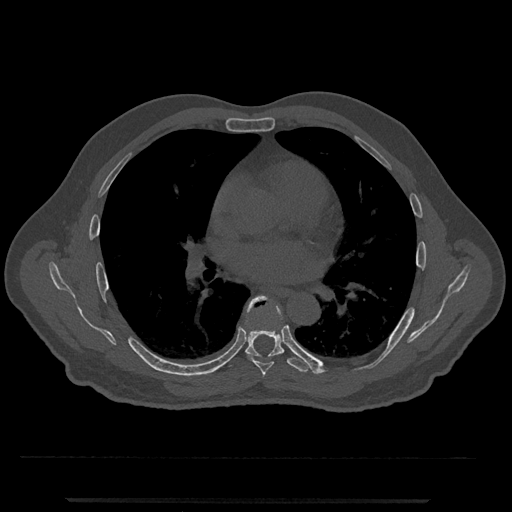
CT including the spine, one axial slice; position 711 of 797 along the scan axis; reconstruction kernel Br40s/3; 120 kVp; bone window (W 1800 / L 400 HU); 512 × 512 image matrix, field of view 419 × 419 mm. Male patient, age 63 years. From the clinical record (not read from this slice): primary cancer: prostate.
Annotated regions visible in this slice (semi-automatic segmentation, software-assisted and operator-edited):
- T6 vertebra: box from (x=245, y=296) to (x=280, y=376) px
- T7 vertebra: (x=221, y=301)–(x=321, y=374)